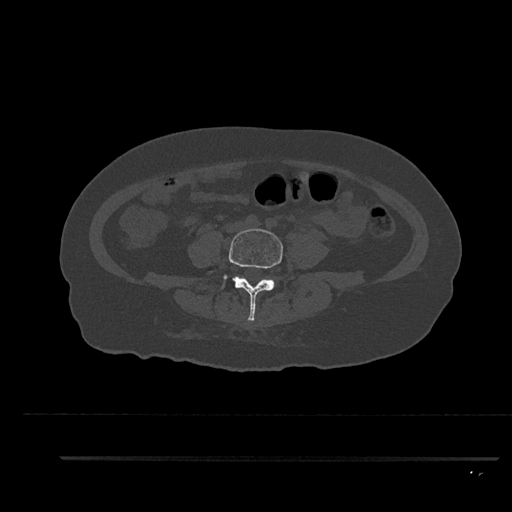
CT including the spine, one axial slice; slice 12 of 797 in the series (ordered by position); reconstruction kernel Br40s/3; bone window (W 1800 / L 400 HU); 0.5 mm slice thickness; 512 × 512 image matrix. Patient: female, 44 years. From the clinical record (not read from this slice): primary cancer: renal; vertebrae with lytic lesions (as recorded): L1.
Structures marked on this image (semi-automatic segmentation, software-assisted and operator-edited):
- L4 vertebra: bounding box [x1, y1, x2, y2] px = [221, 228, 283, 321]